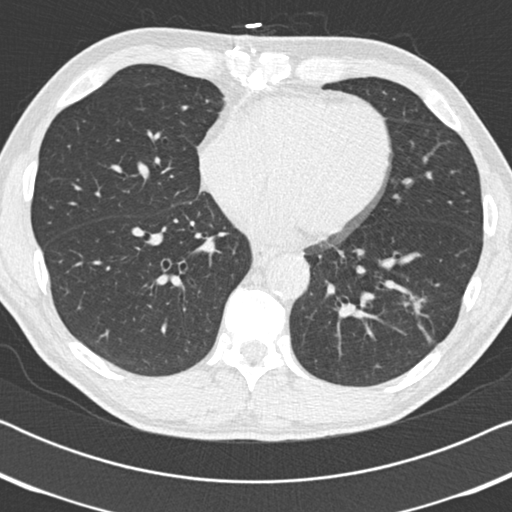
Chest CT (low-dose screening protocol), one axial image; third screening round (two years after baseline); lung window (W 1500 / L -600 HU); standard (soft-tissue) reconstruction kernel (B30f); slice 114 of 186 in the series; 512 × 512 image matrix, field of view 330 × 330 mm. Male, age 59 years at enrolment. Current smoker at enrolment.
Expert-annotated lung lesion, bounding box (x1, y1, x2, y2) in pixels: (389, 279, 456, 343). The screening reader recorded 2 non-calcified nodules or masses ≥4 mm on this exam; which of them this box marks is not recorded. Lung cancer was diagnosed 73 days after this screen: adenocarcinoma, NOS, left lower lobe, poorly differentiated (G3), stage IA (AJCC 6th edition), 20 mm at pathology.